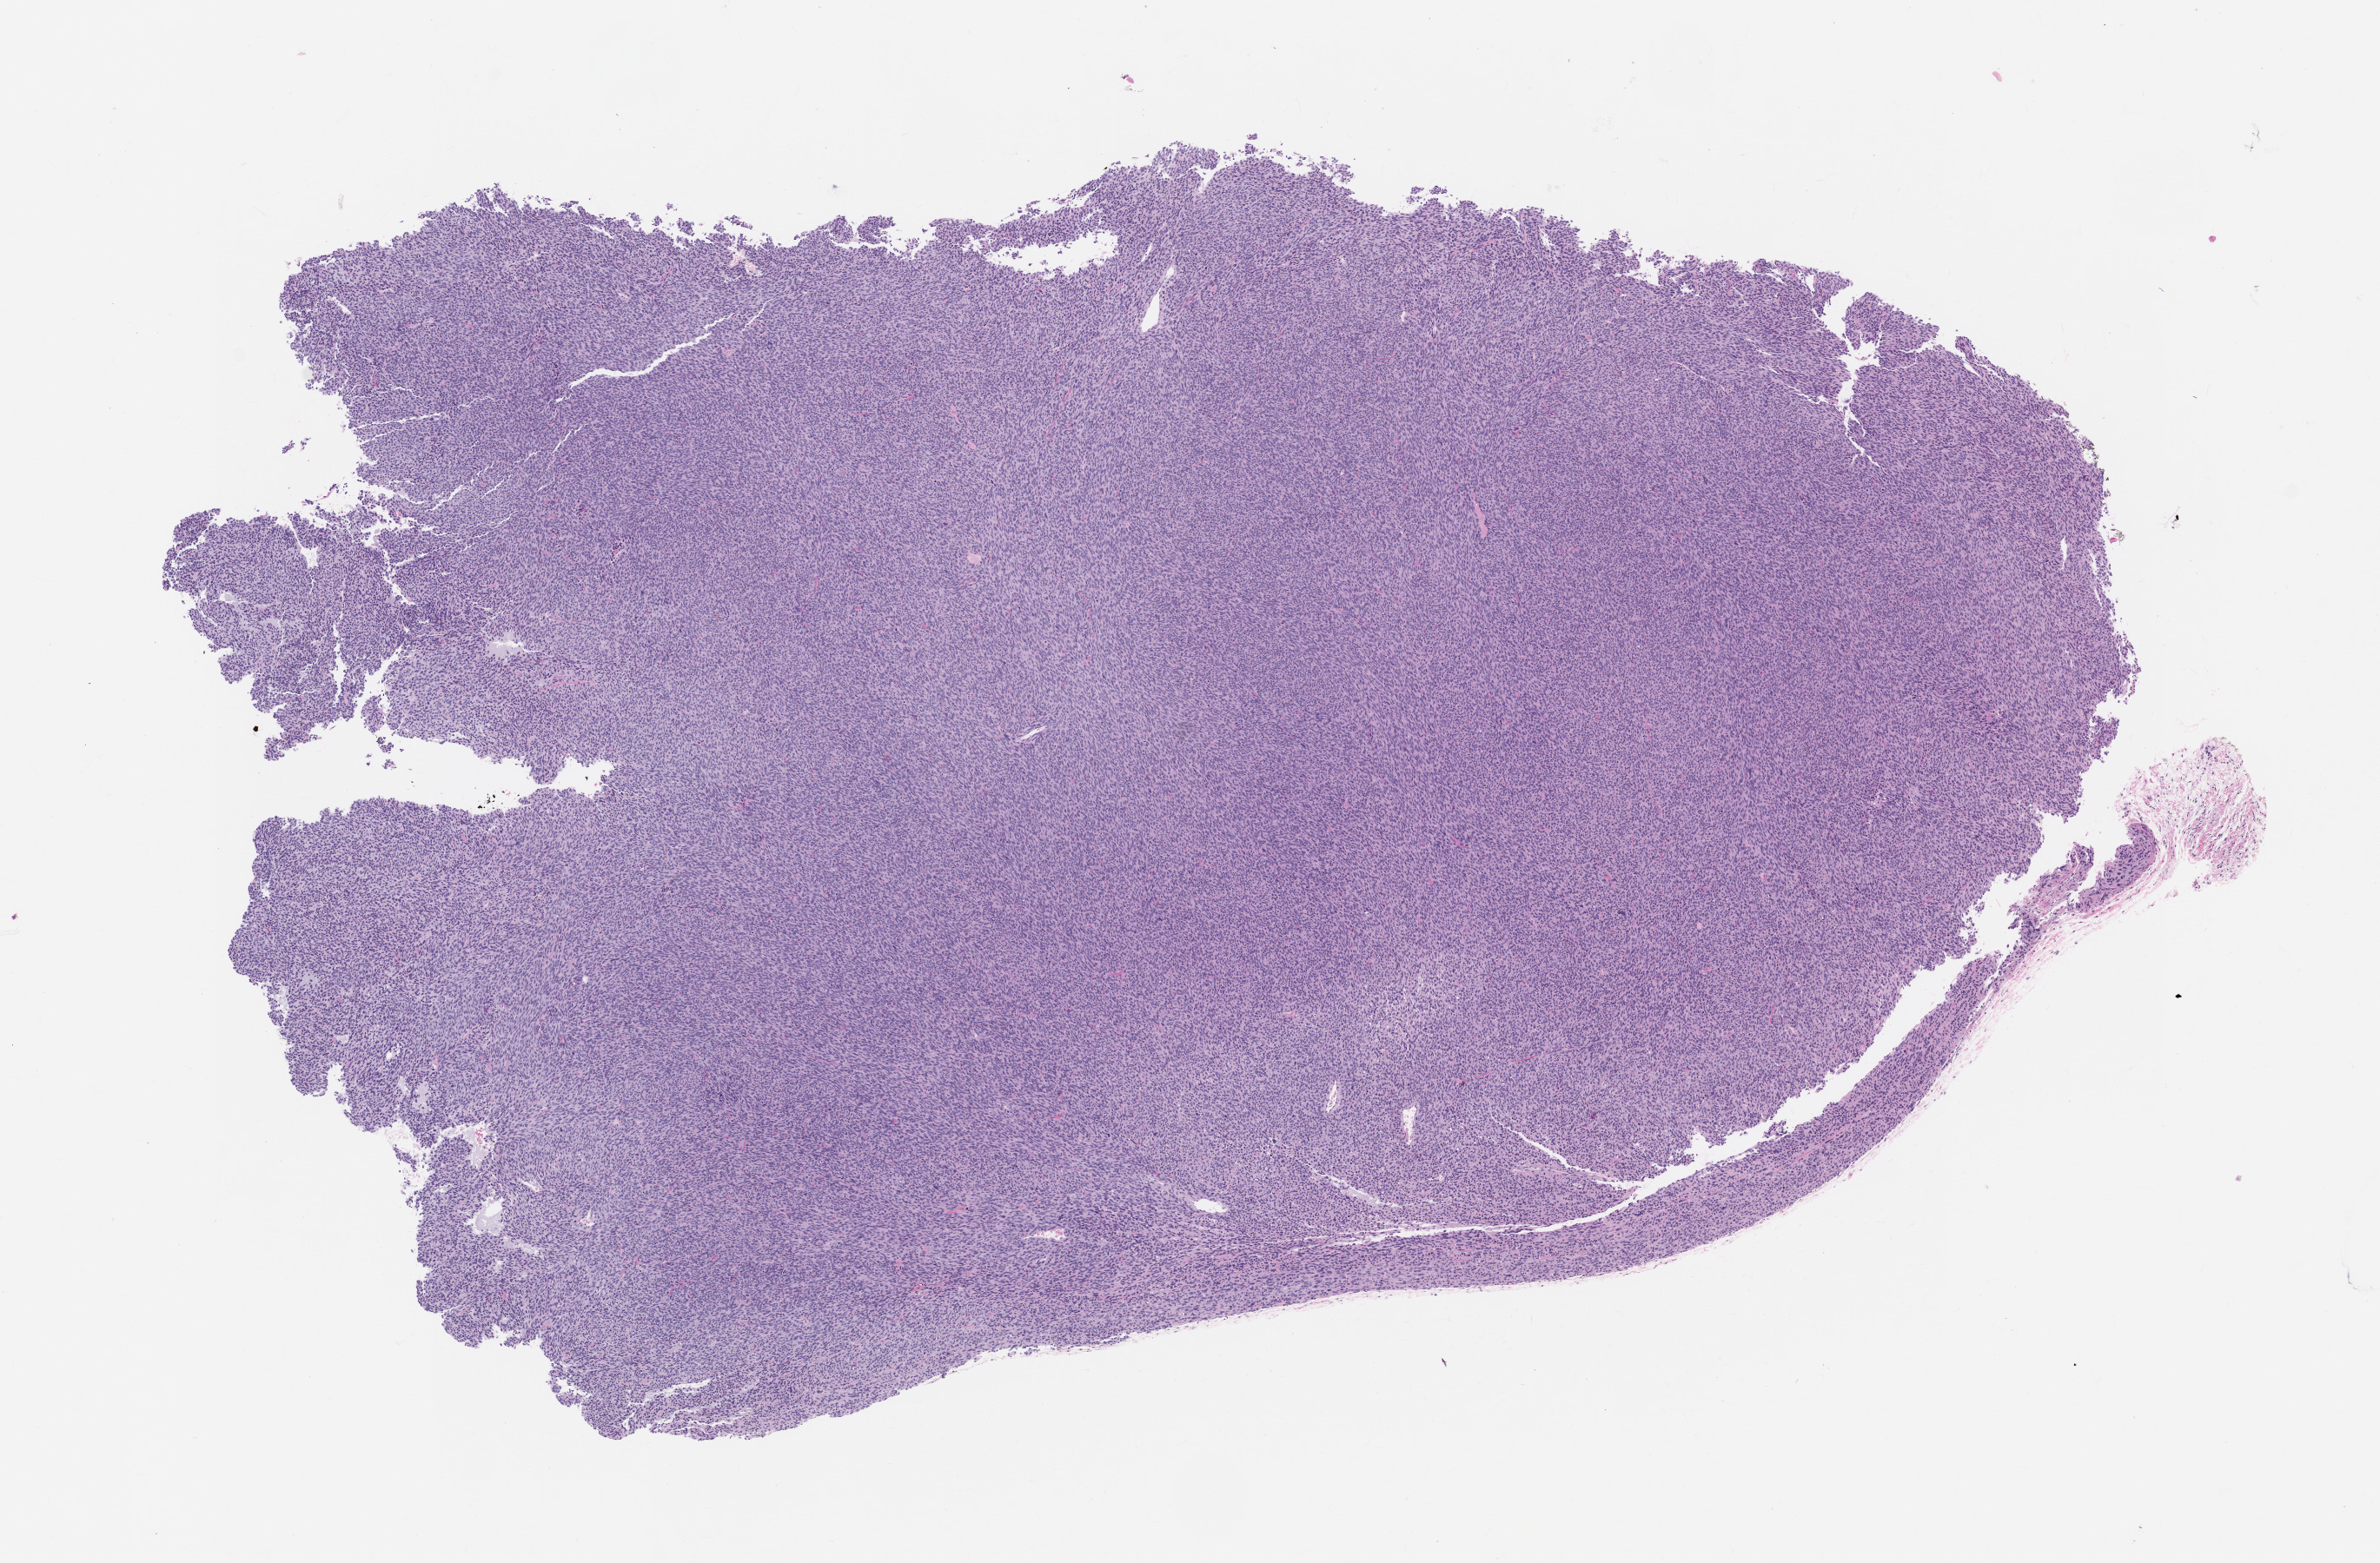
H&E whole-slide image of a patient-derived xenograft (PDX) tumor grown in a mouse, passage 2, whole scanned area (about 11.0 x 7.2 mm) shown as a low-resolution overview. FFPE section. Originating tumor site category: uterus.
• originating patient diagnosis: Leiomyosarcoma